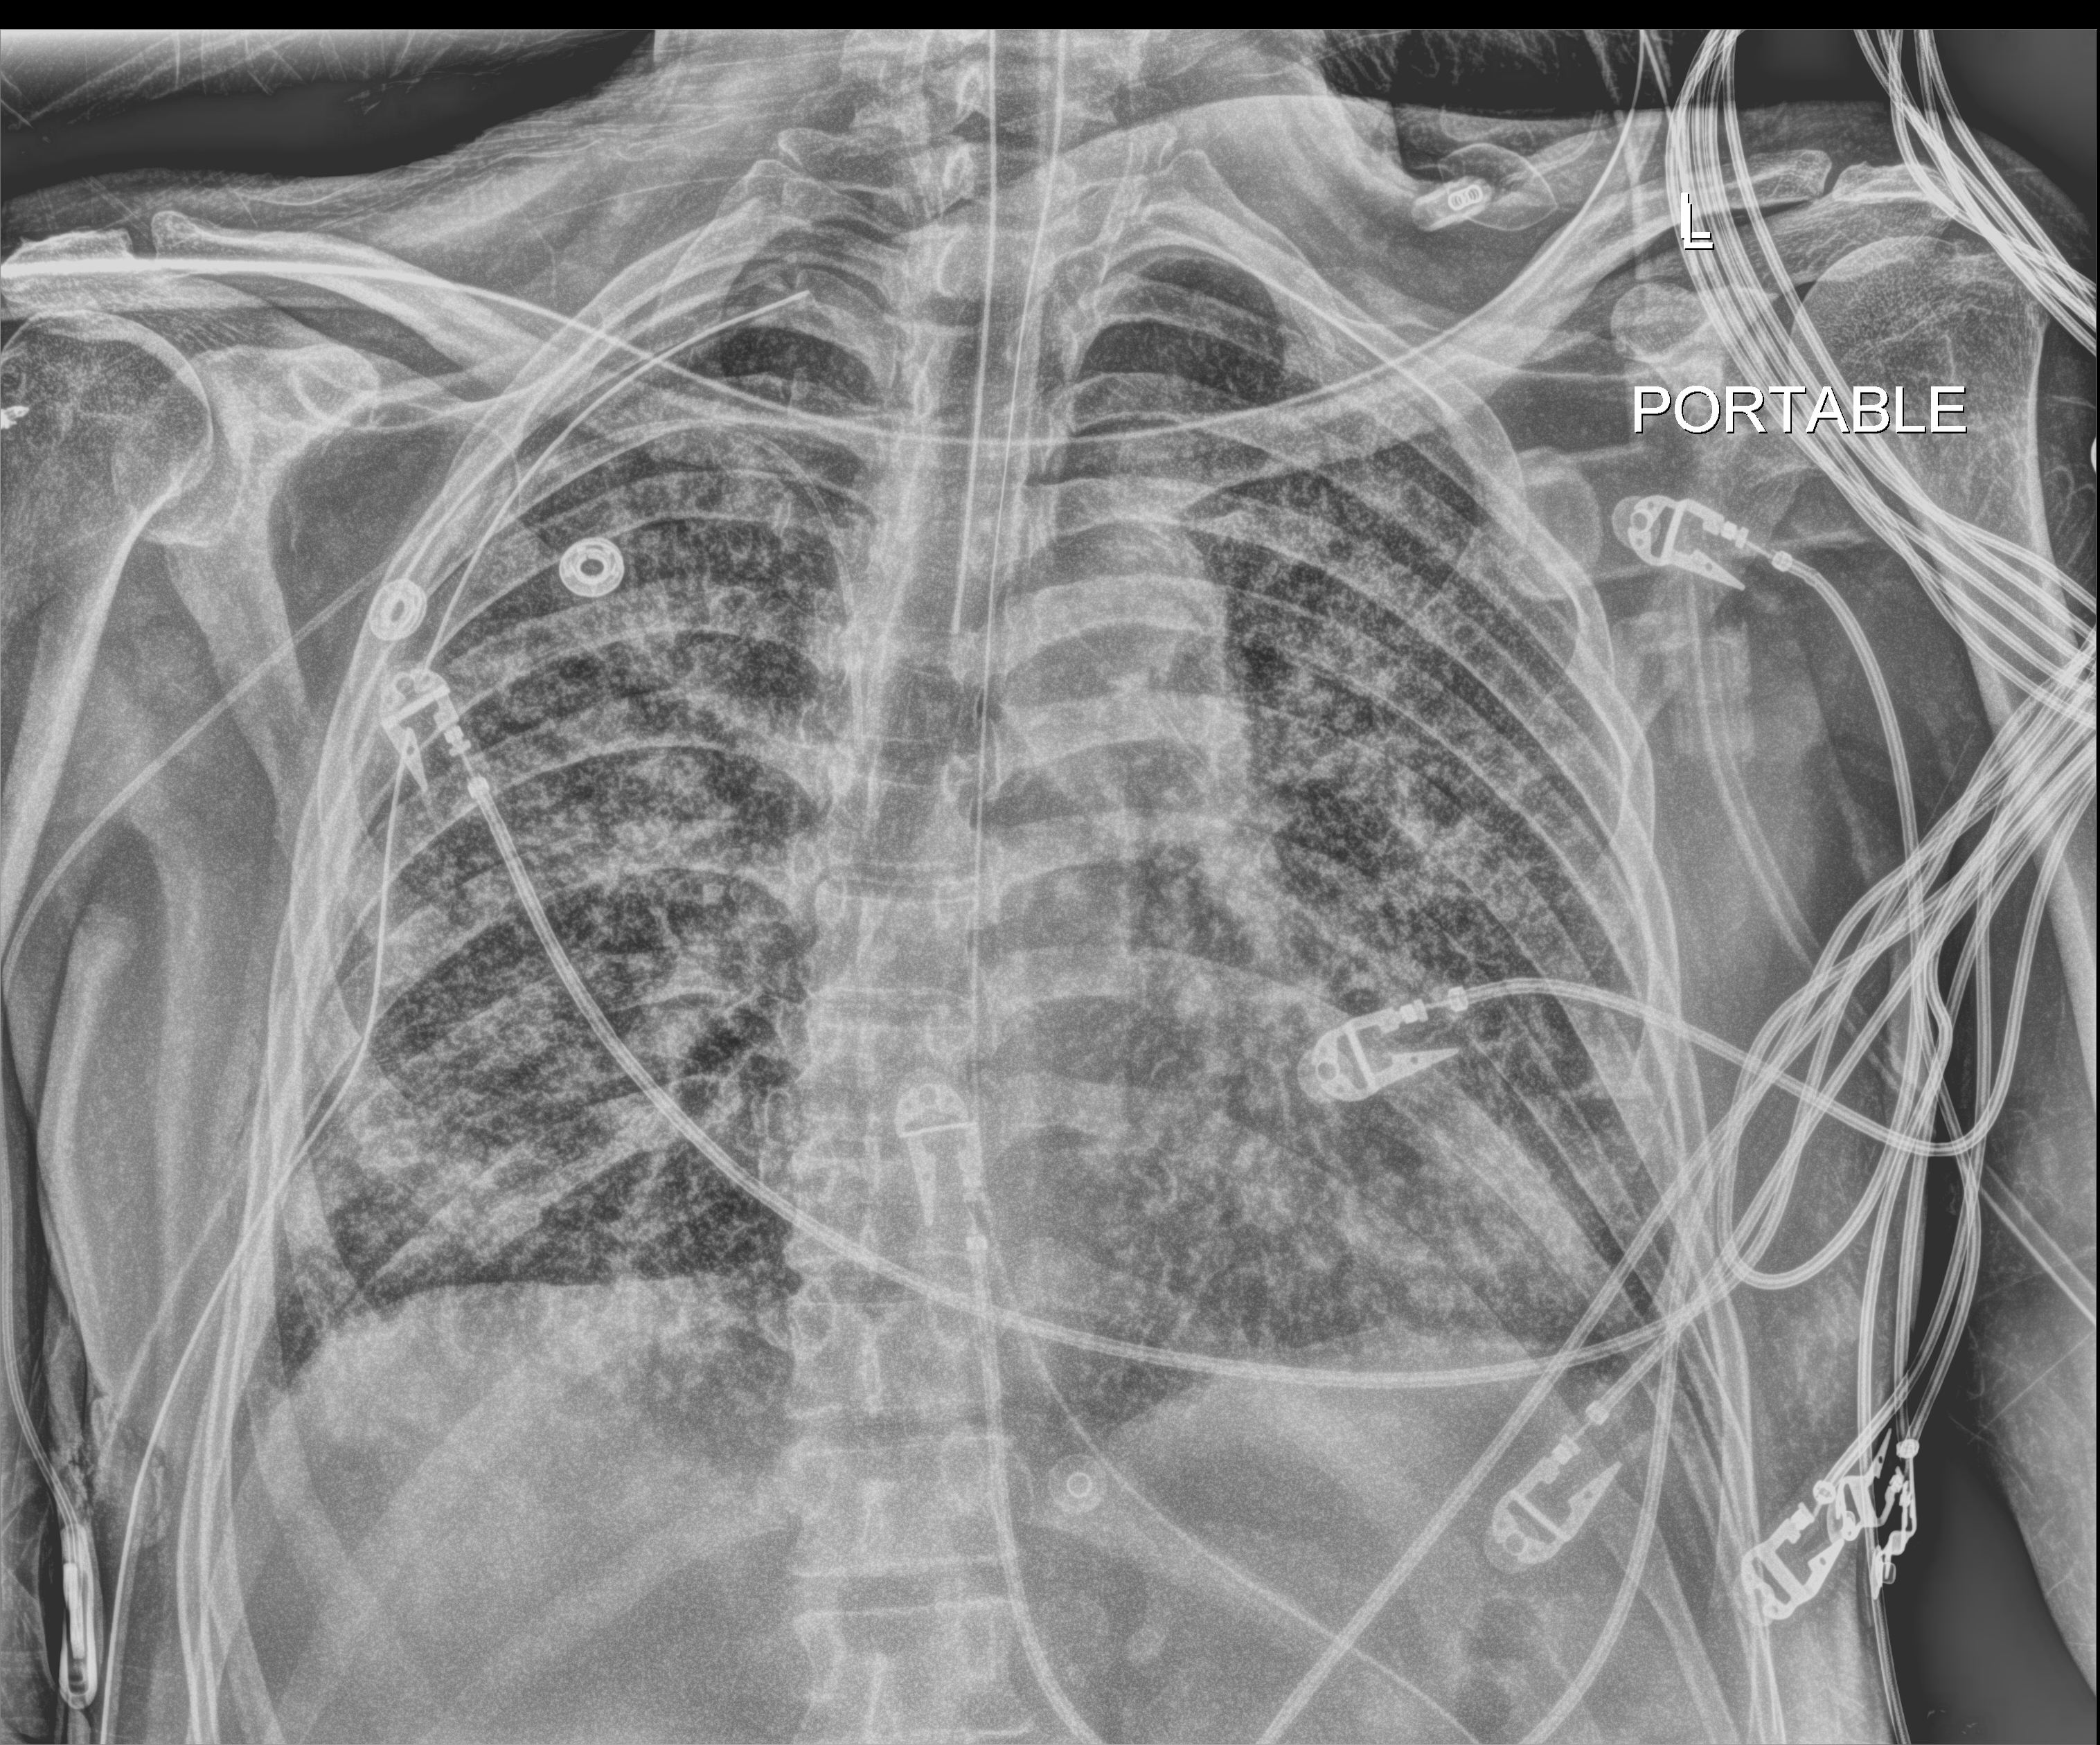
Chest radiograph (digital radiography); anteroposterior (AP) projection. Patient hospitalised with COVID-19; male, aged 60–74 years.
Hospital-stay facts (about this admission, not read from this image; timing relative to this image not recorded): mechanically ventilated during this hospital stay: yes.